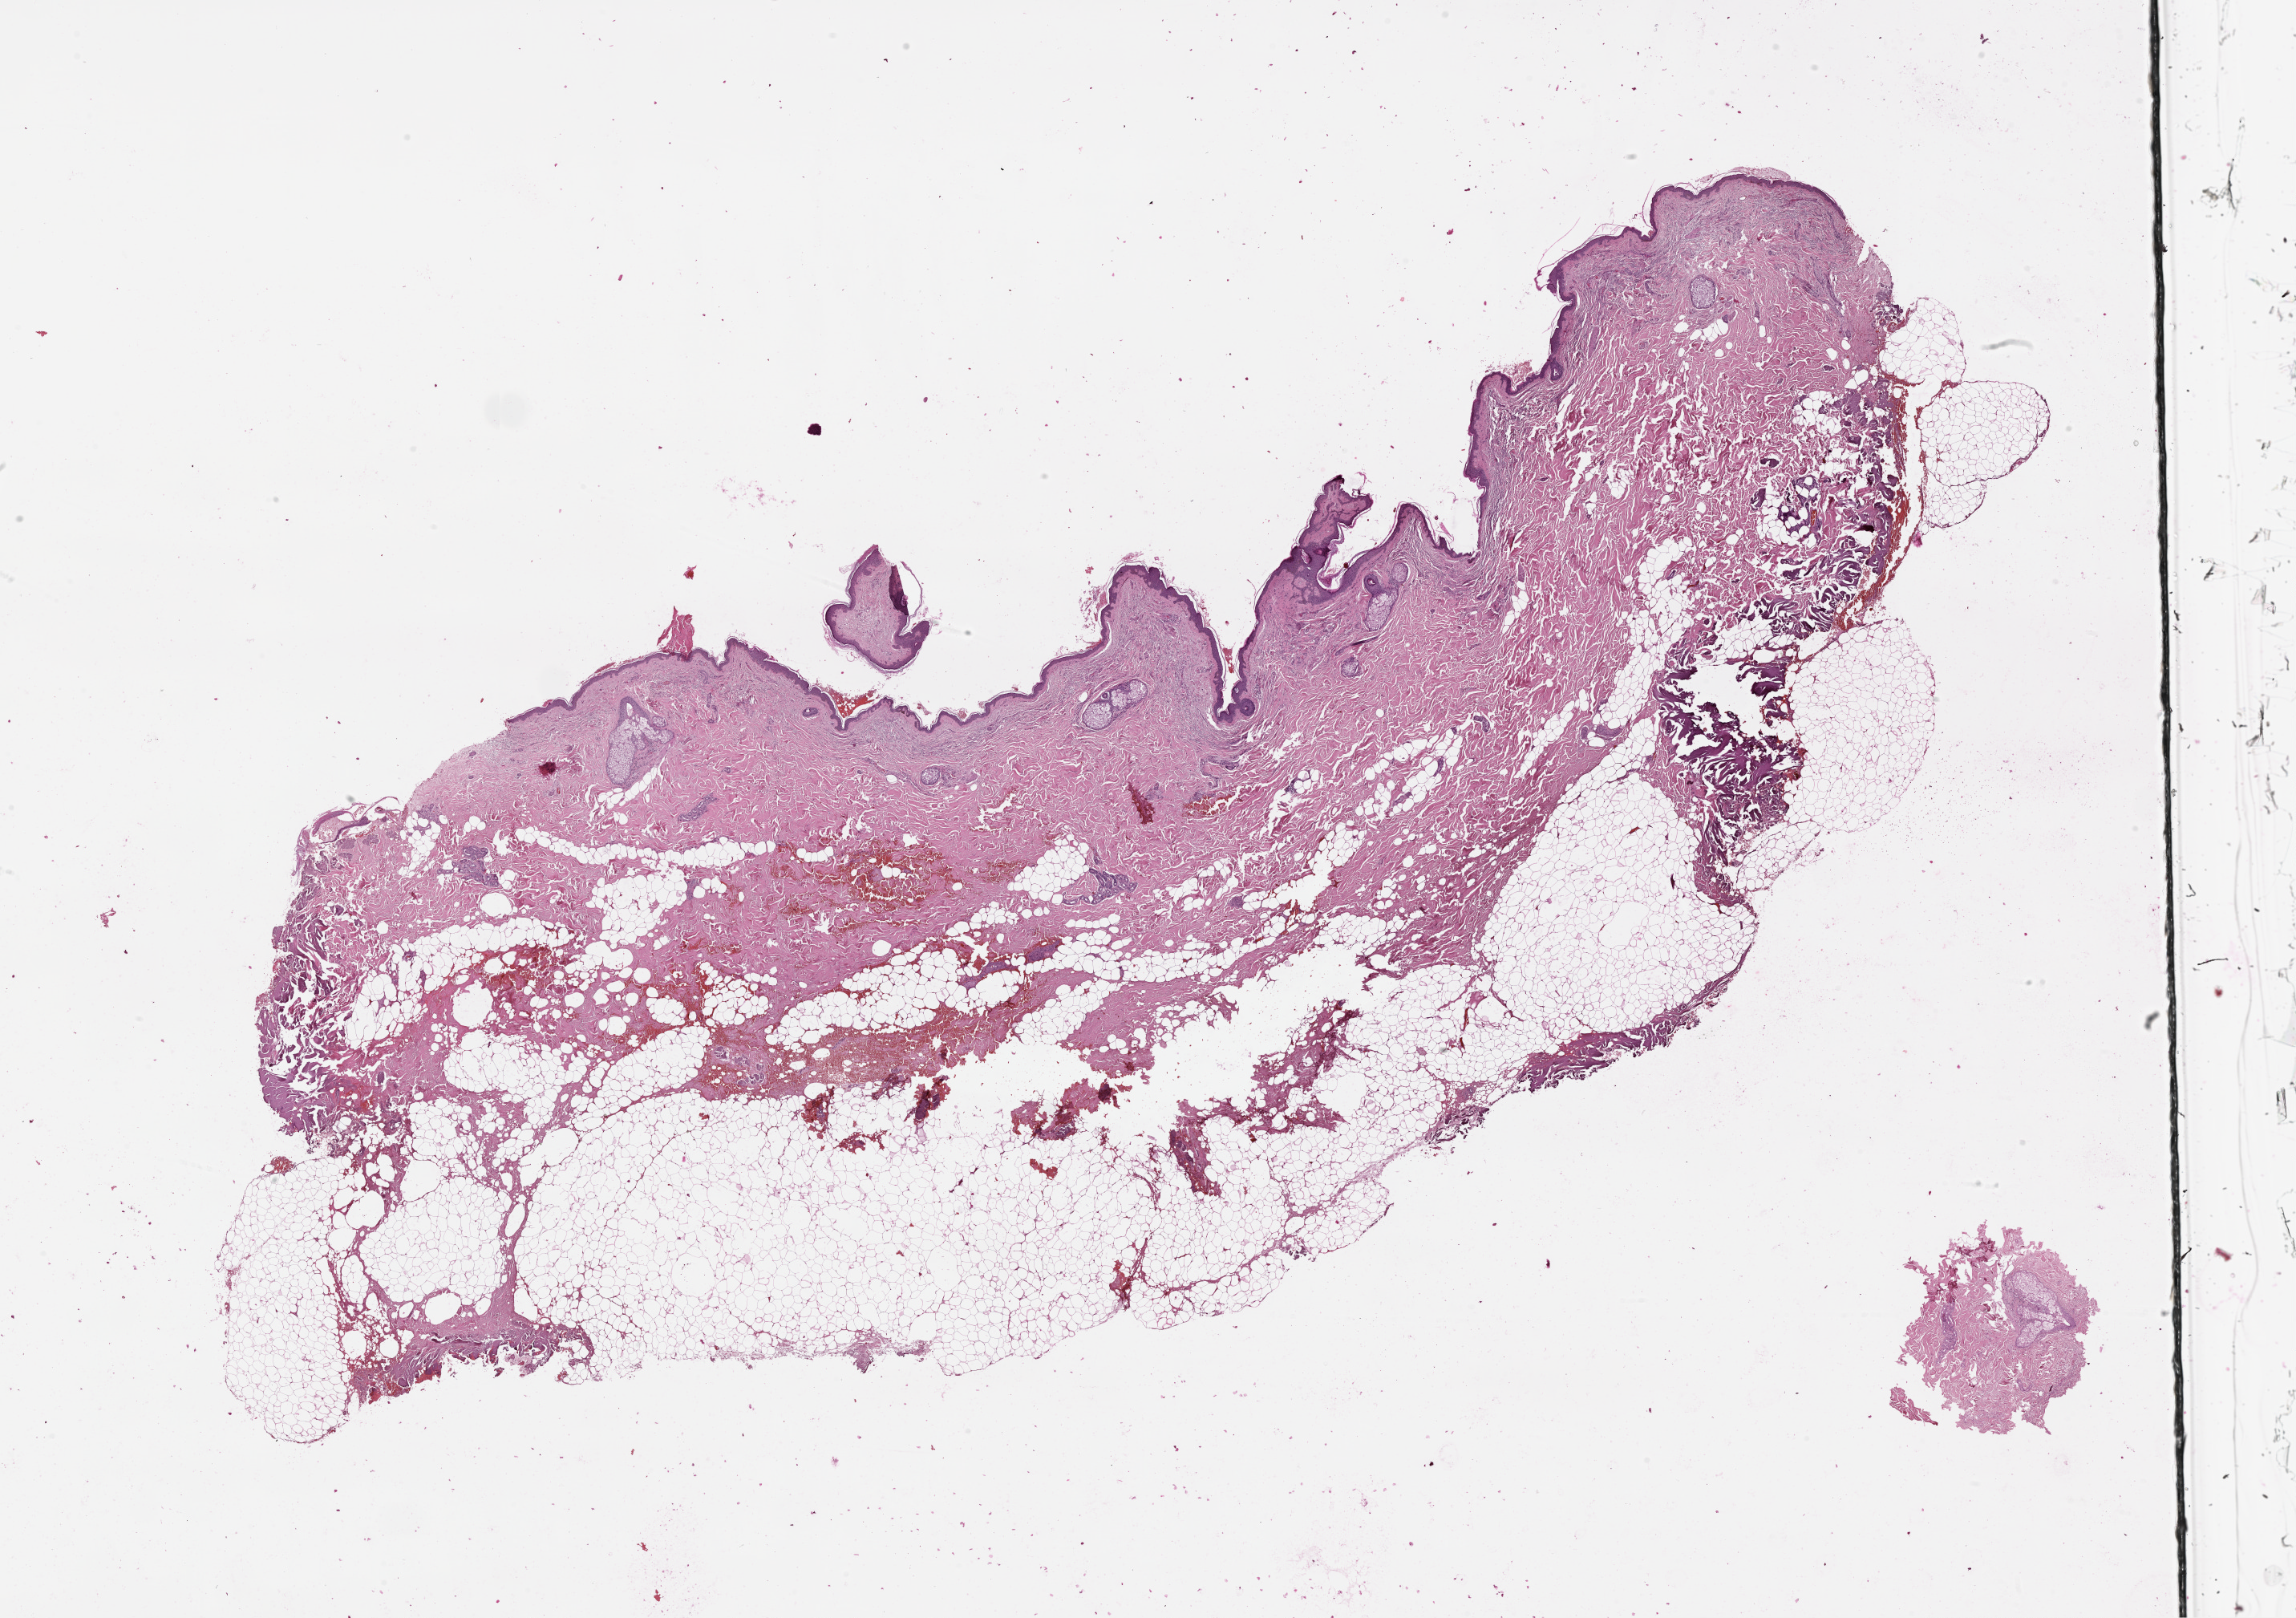
Digitized Hematoxylin and eosin (H&E) stained tissue section (whole slide) — shown as a low-resolution overview of the whole scanned area (about 23.1 x 16.2 mm, slide scanned at 20x). Normal (non-tumour) tissue sample, sampled site: shoulder. 68-year-old female patient.
• this section: normal (non-tumour) tissue from the same patient
• patient diagnosis: Malignant melanoma, NOS